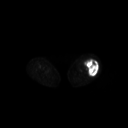
FDG PET of an extremity soft-tissue mass (from a PET/CT study), one axial slice. Position 211 of 267 along the scan axis. 3.27 mm slice thickness. 128 × 128 image matrix. Patient: female, 62 years. Case-level facts recorded for this patient, not image findings: histological type: undifferentiated – high grade; grade: high; site of the primary tumour: left thigh.
Annotated regions visible in this slice (expert contour drawn on MRI and transferred to this co-registered scan by the dataset authors):
- gross tumour volume including surrounding oedema: bounding box [x1, y1, x2, y2] px = [83, 59, 99, 76]
- gross tumour volume (mass): [85, 59, 98, 76]